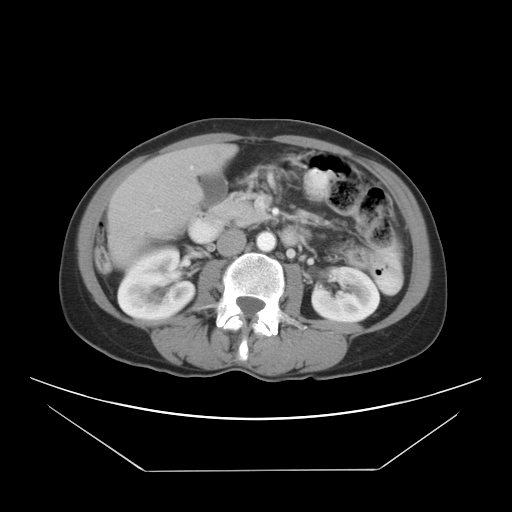
Contrast-enhanced abdominal CT, one axial slice. Position 10 of 30 along the scan axis. Intravenous contrast given. Soft-tissue window (W 400 / L 40 HU). 7.5 mm slice thickness. 512 × 512 image matrix. Female patient, age 54 years. Case-level facts recorded for this patient, not image findings: diagnosis: colorectal cancer liver metastases, imaged before liver resection; multiple liver metastases: yes.
Annotated regions visible in this slice (expert manual segmentation):
- liver: bounding box <109,146,231,261> (left, top, right, bottom; pixels)
- planned liver remnant (the part of the liver to remain after resection): <123,146,231,219>
- portal vein (with intrahepatic branches): <155,165,195,212>
- liver metastasis: <117,223,124,233>